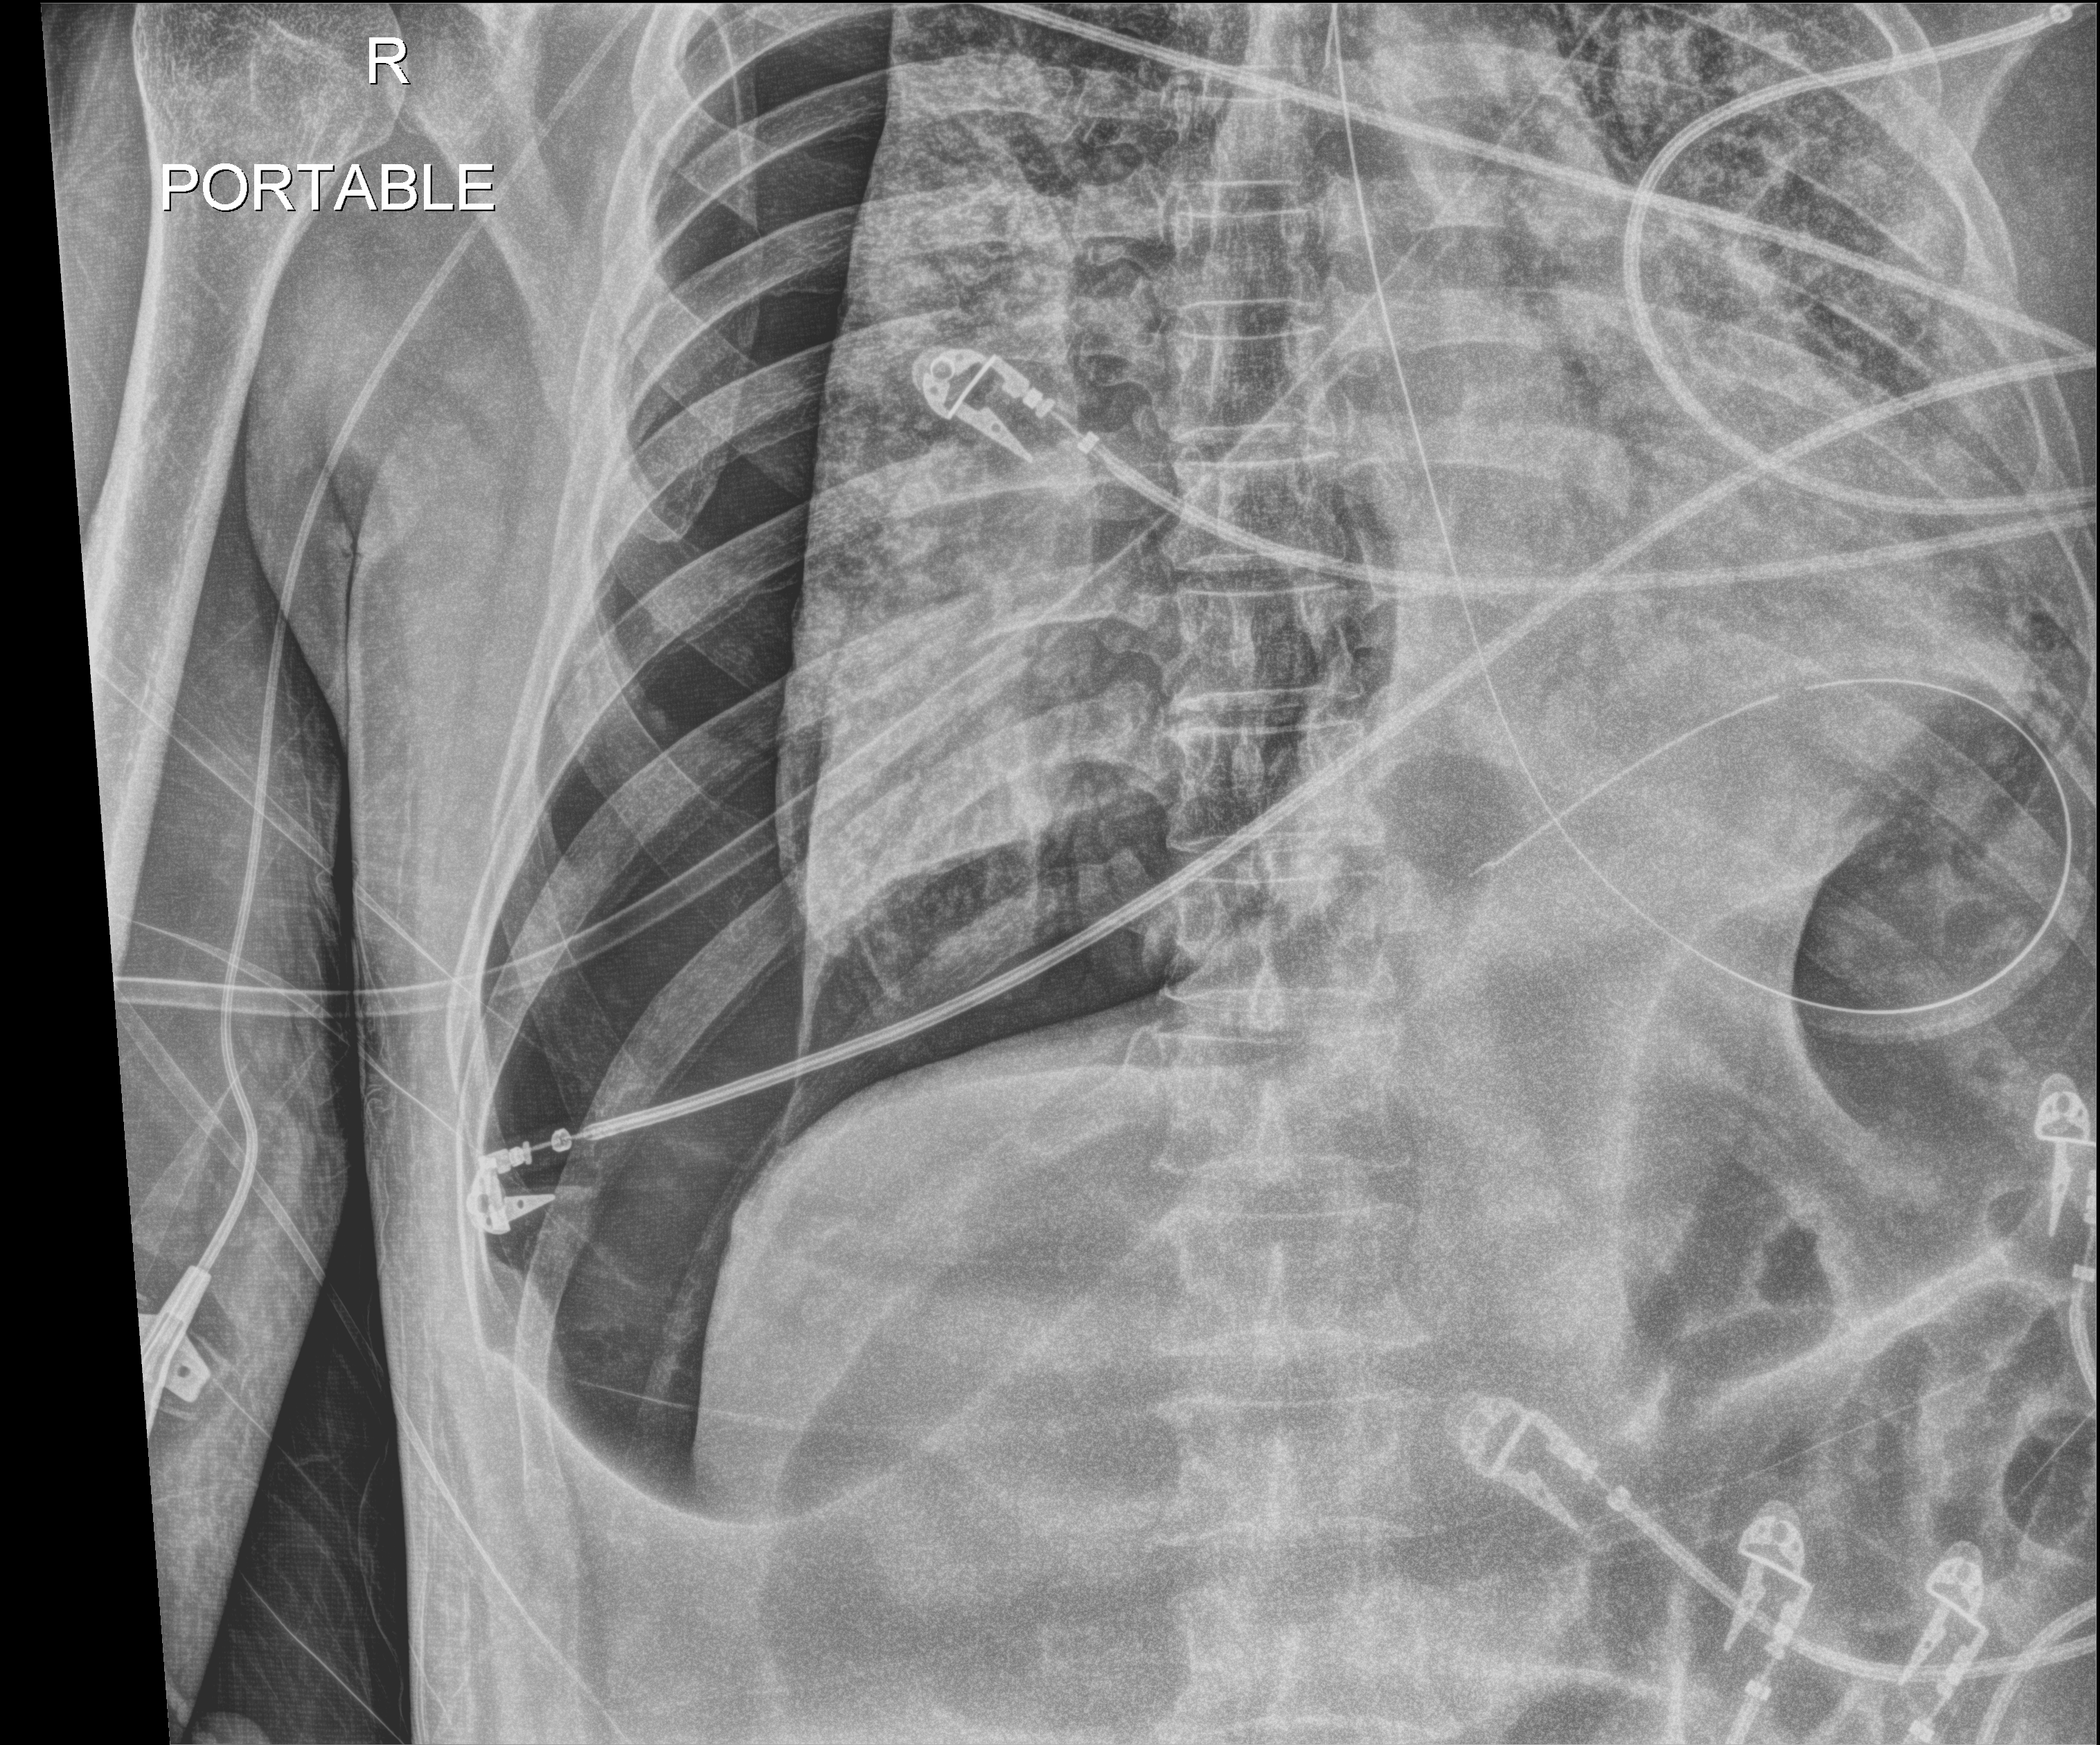
Chest radiograph. Patient hospitalised with COVID-19; male, aged 60–74 years.
Hospital-stay facts (about this admission, not read from this image; timing relative to this image not recorded): mechanically ventilated during this hospital stay: yes; other chronic lung disease (admission record): no; admitted to intensive care during this hospital stay: yes.